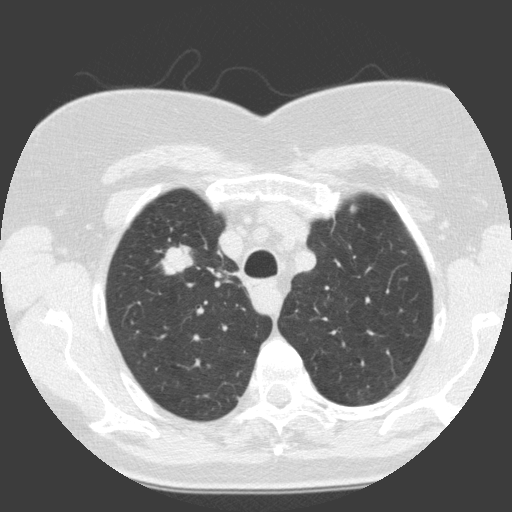
Chest CT (low-dose screening protocol), one axial image. Baseline screening round. Lung window (W 1500 / L -600 HU). 2 mm slice thickness. Standard (soft-tissue) reconstruction kernel (C). 120 kVp. Slice 30 of 146 in the series. Female, age 68 years at enrolment.
Lesion marked by an expert reader, bounding box (x1, y1, x2, y2) in pixels: (154, 242, 200, 285). The exam's reader record, not a measurement of the box and not confirmed to be the same lesion: non-calcified nodule or mass ≥4 mm, right upper lobe, 19 × 12 mm, smooth margins, soft tissue attenuation. Lung cancer was diagnosed 30 days after this screen: squamous cell carcinoma, NOS, right upper lobe, moderately differentiated (G2), stage IA (AJCC 6th edition), 28 mm at pathology.